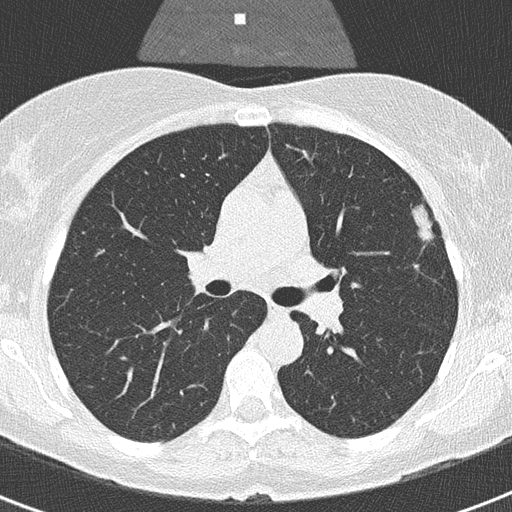
Low-dose screening chest CT, one axial slice. Position 206 of 320 along the scan axis. 120 kVp. Lung window (W 1500 / L -600 HU). 2 mm slice thickness. 512 × 512 image matrix, field of view 290 × 290 mm.
Annotated regions visible in this slice (manually delineated by an expert):
- lesion 1 (tumor, upper lobe of left lung): bounding box (x1, y1, x2, y2) in pixels: (412, 204, 433, 241)